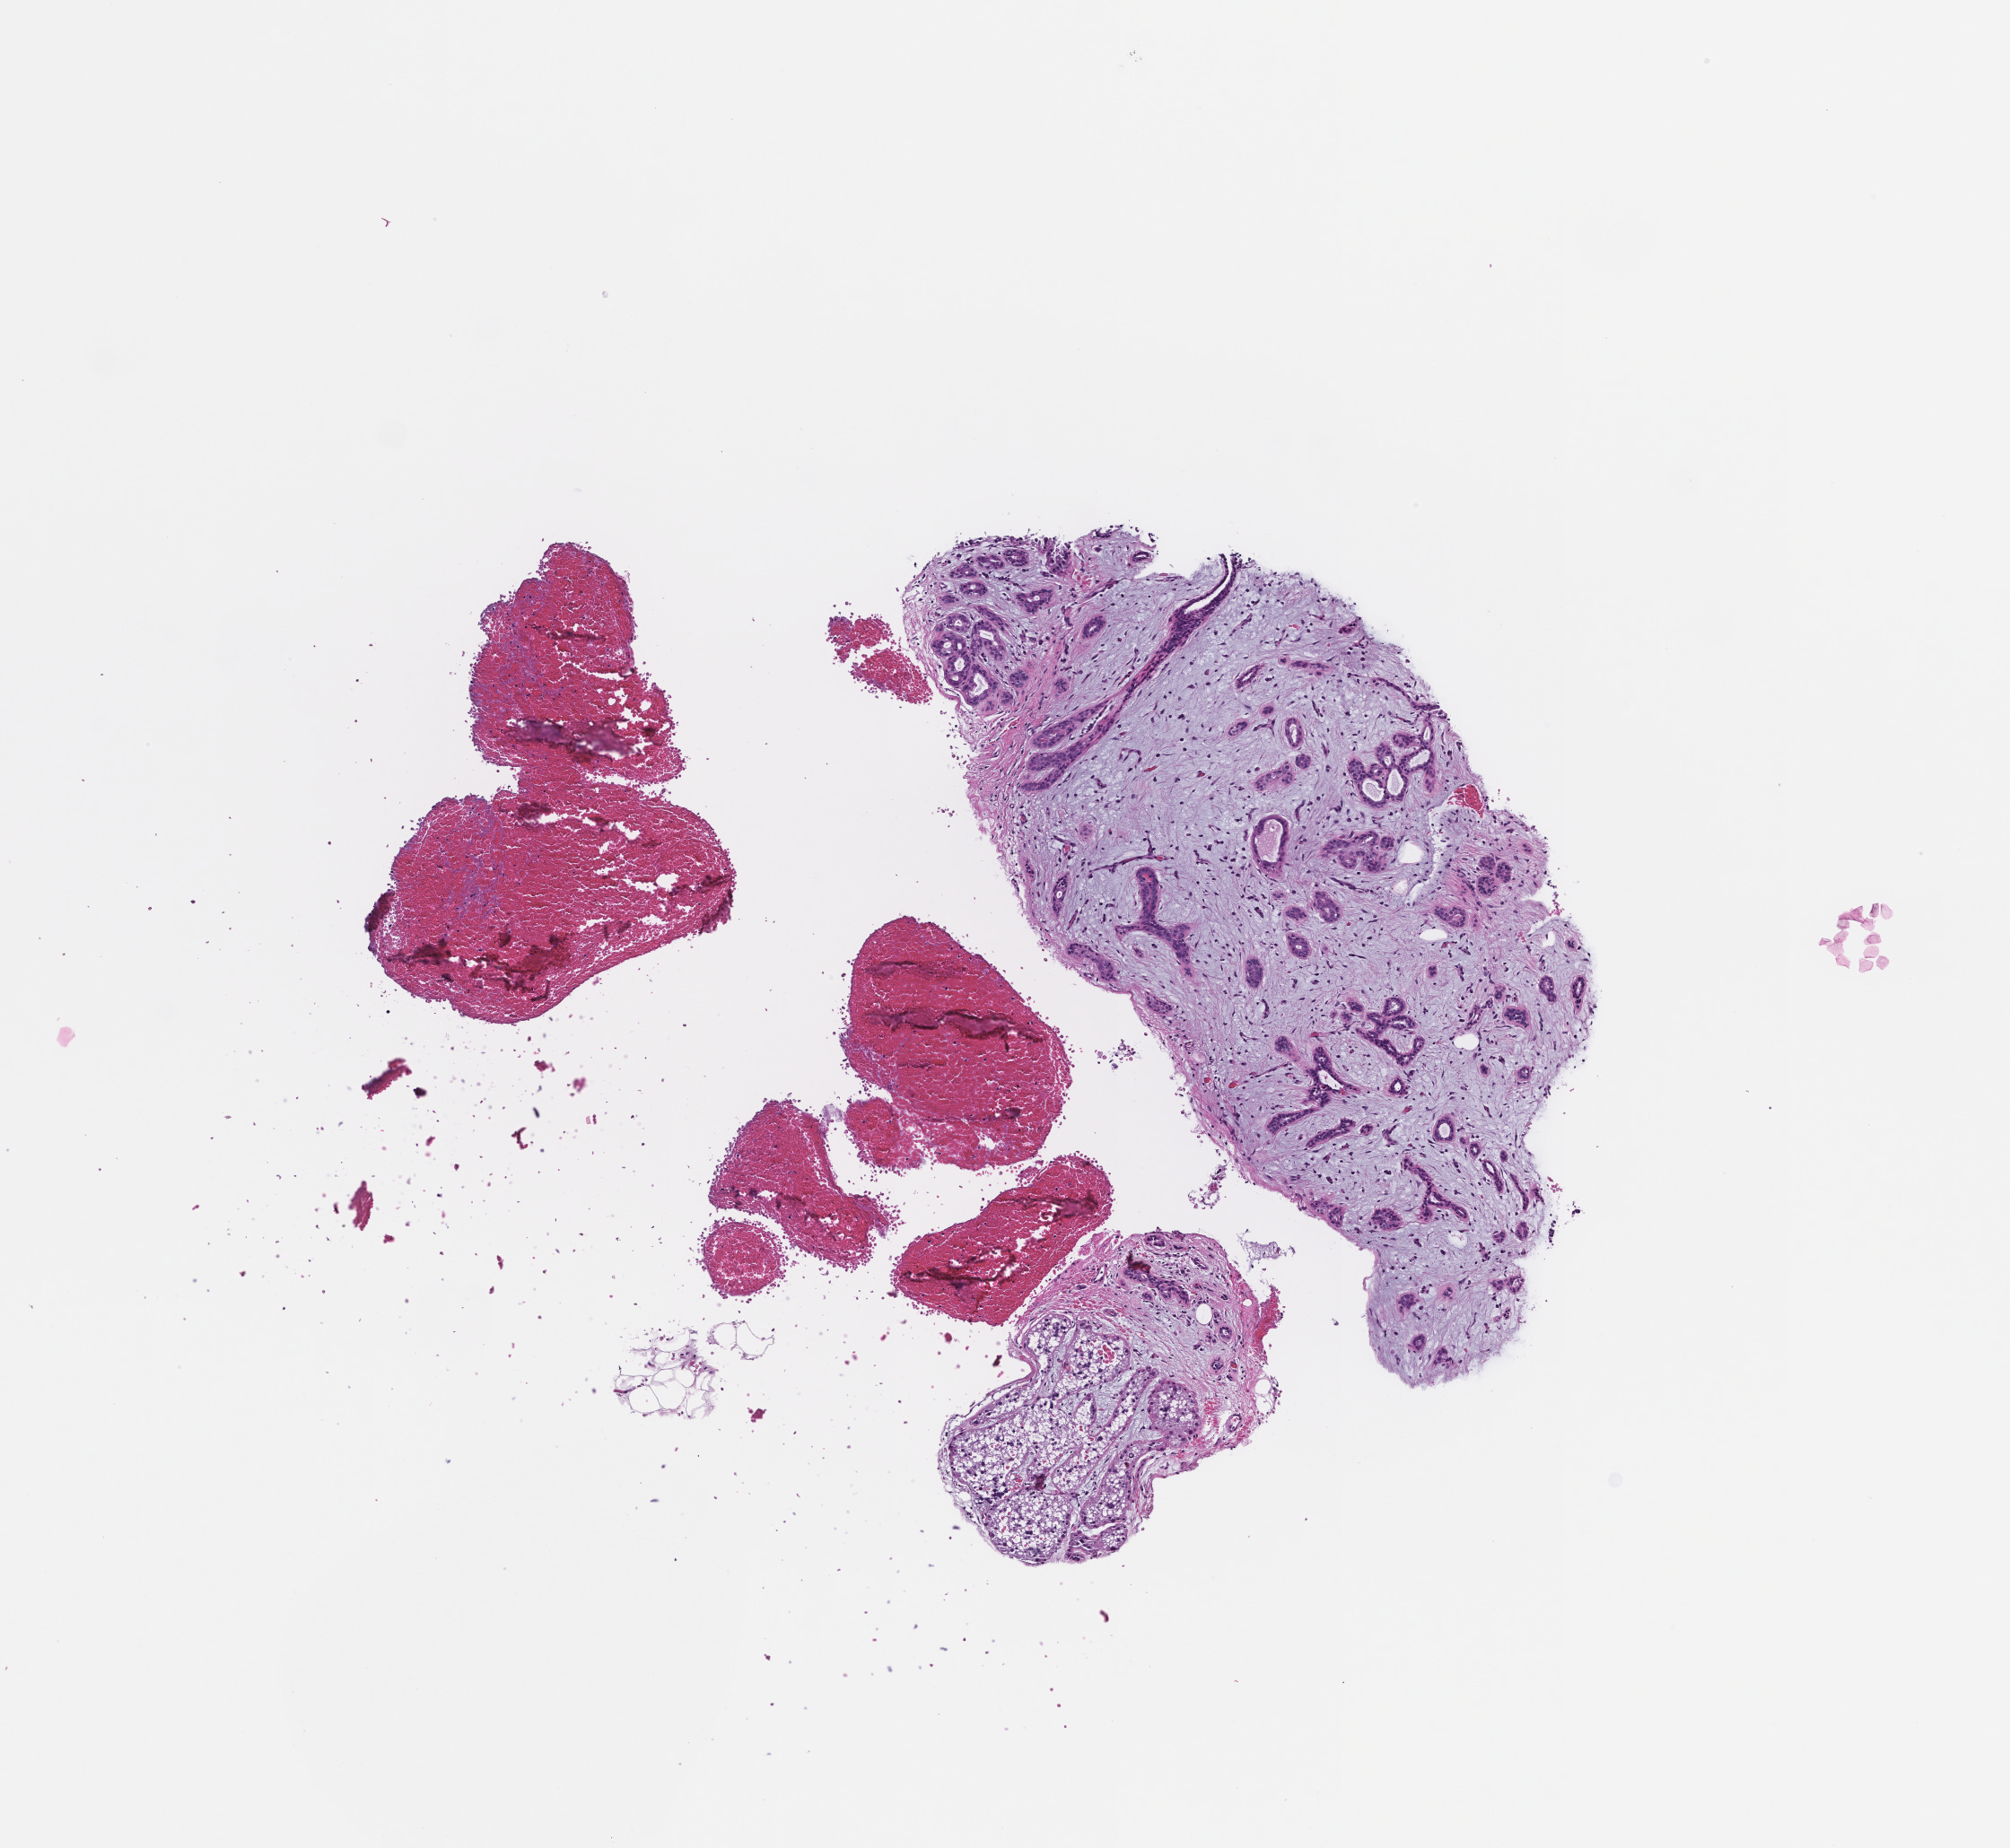
Digitized hematoxylin and eosin (H&E)-stained section — shown as a low-resolution overview of the whole scanned area (about 4.5 x 4.2 mm), formalin-fixed, paraffin-embedded (FFPE) tissue, tissue site: ovary, collected at baseline (before treatment). Female patient.
This section: primary tumour tissue. Diagnosis: Ovarian Carcinoma.